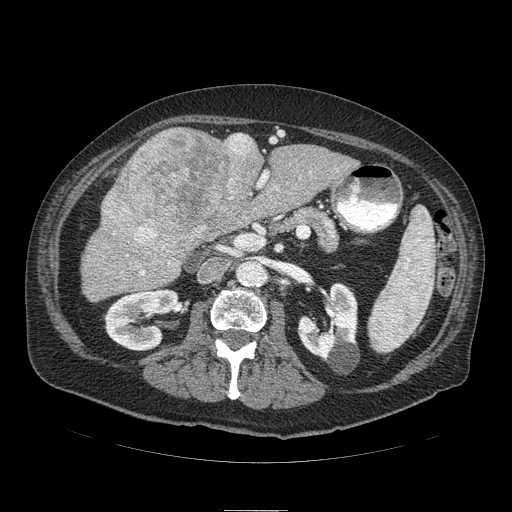
Contrast-enhanced abdominal CT (liver protocol), one axial slice; position 37 of 103 along the scan axis; reconstruction kernel STANDARD; 120 kVp; soft-tissue window (W 400 / L 40 HU); 2.5 mm slice thickness; 512 × 512 image matrix. Case-level facts recorded for this patient, not image findings: diagnosis: hepatocellular carcinoma (patient treated with transarterial chemoembolisation; whether this scan precedes or follows treatment is not stated here); TNM stage (as recorded): Stage-IIIA; Child-Pugh class: B; tumour differentiation: well differentiated; tumour nodularity: multinodular.
Structures marked on this image (semi-automatically segmented with operator editing):
- liver parenchyma outside the tumour (the mass and vessels are separate outlines, so this box may not span the whole liver): bounding box <82,128,358,300> (left, top, right, bottom; pixels)
- mass: <102,127,261,254>
- liver vessels: <126,171,268,275>